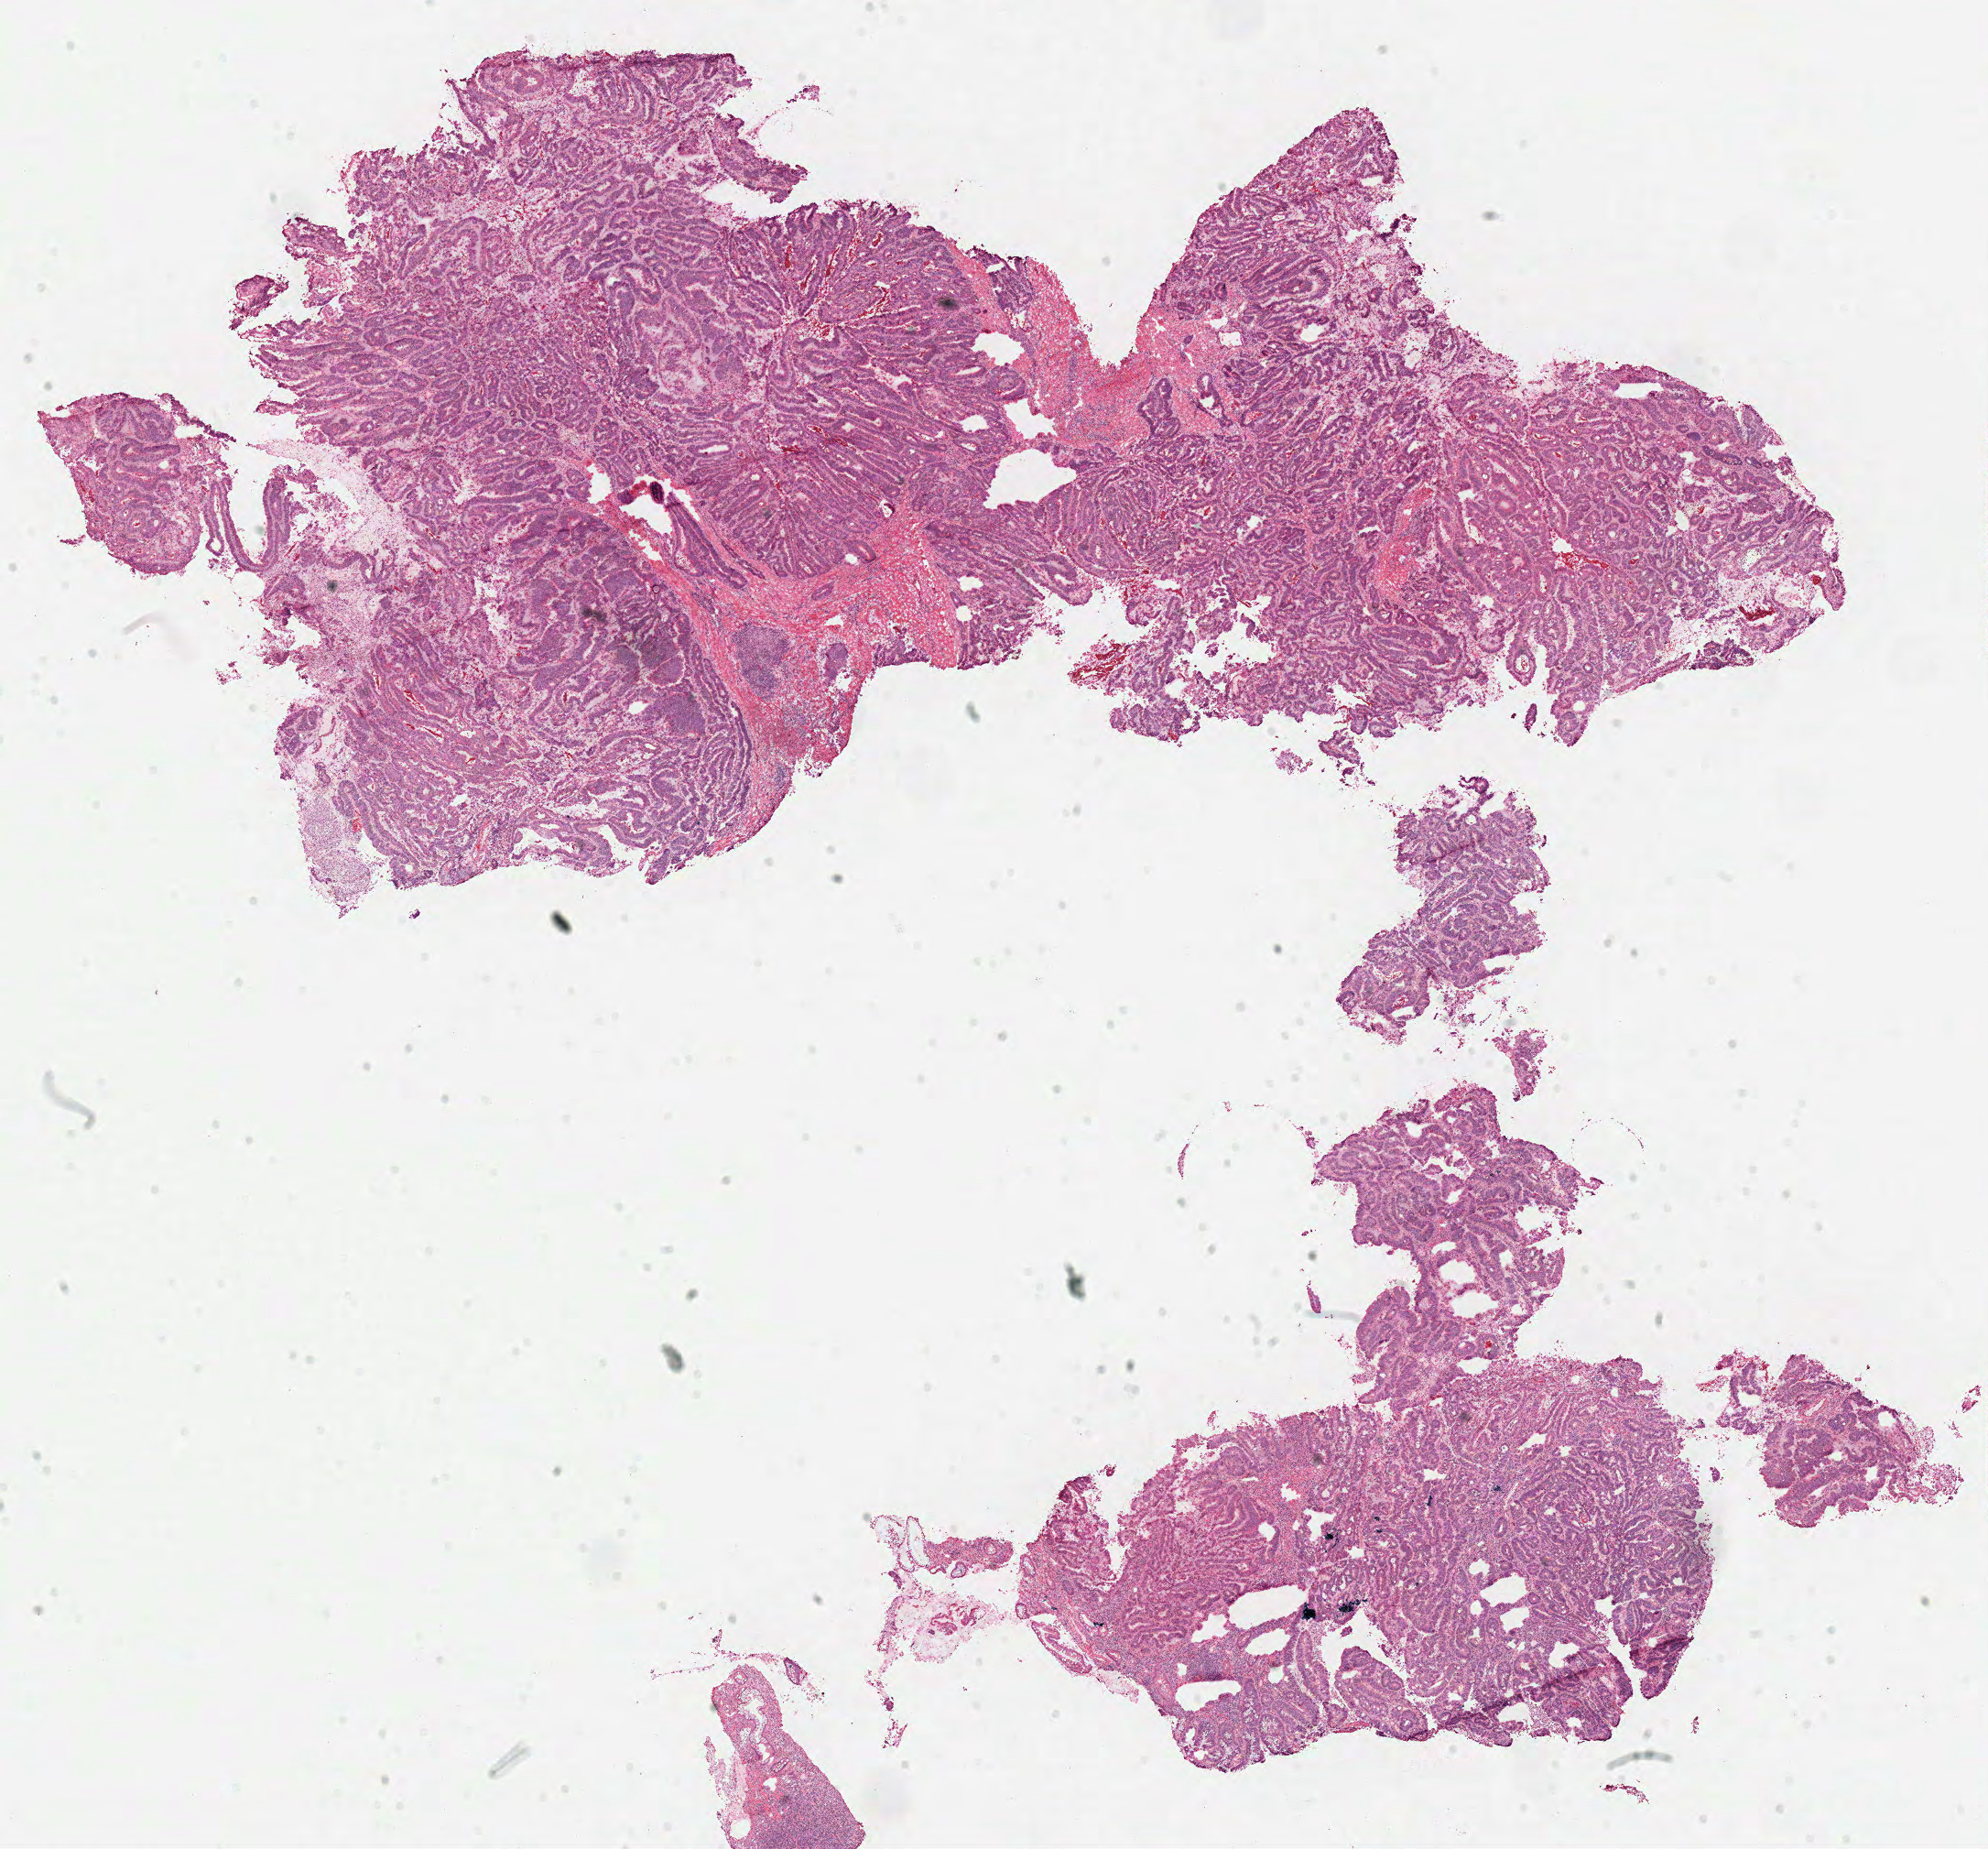
H&E whole-slide image — low-resolution overview of the scanned area, about 17.1 x 15.9 mm (from a 40x scan); frozen section from the top of the tissue portion; primary tumour sample from the colon. Male, age 60 years at initial diagnosis. Pathologist review of this section (percent, as recorded): tumour cells 99%, tumour nuclei 80%, normal cells 0%, stromal cells 0%, necrosis 1%. Infiltration values recorded for this section: lymphocyte infiltration 5%, monocyte infiltration 2%, neutrophil infiltration 5%.
- AJCC pathologic stage: I
- lymph nodes positive (case pathology): 0 of 33 examined
- histologic diagnosis: Adenocarcinoma, NOS (cecum)